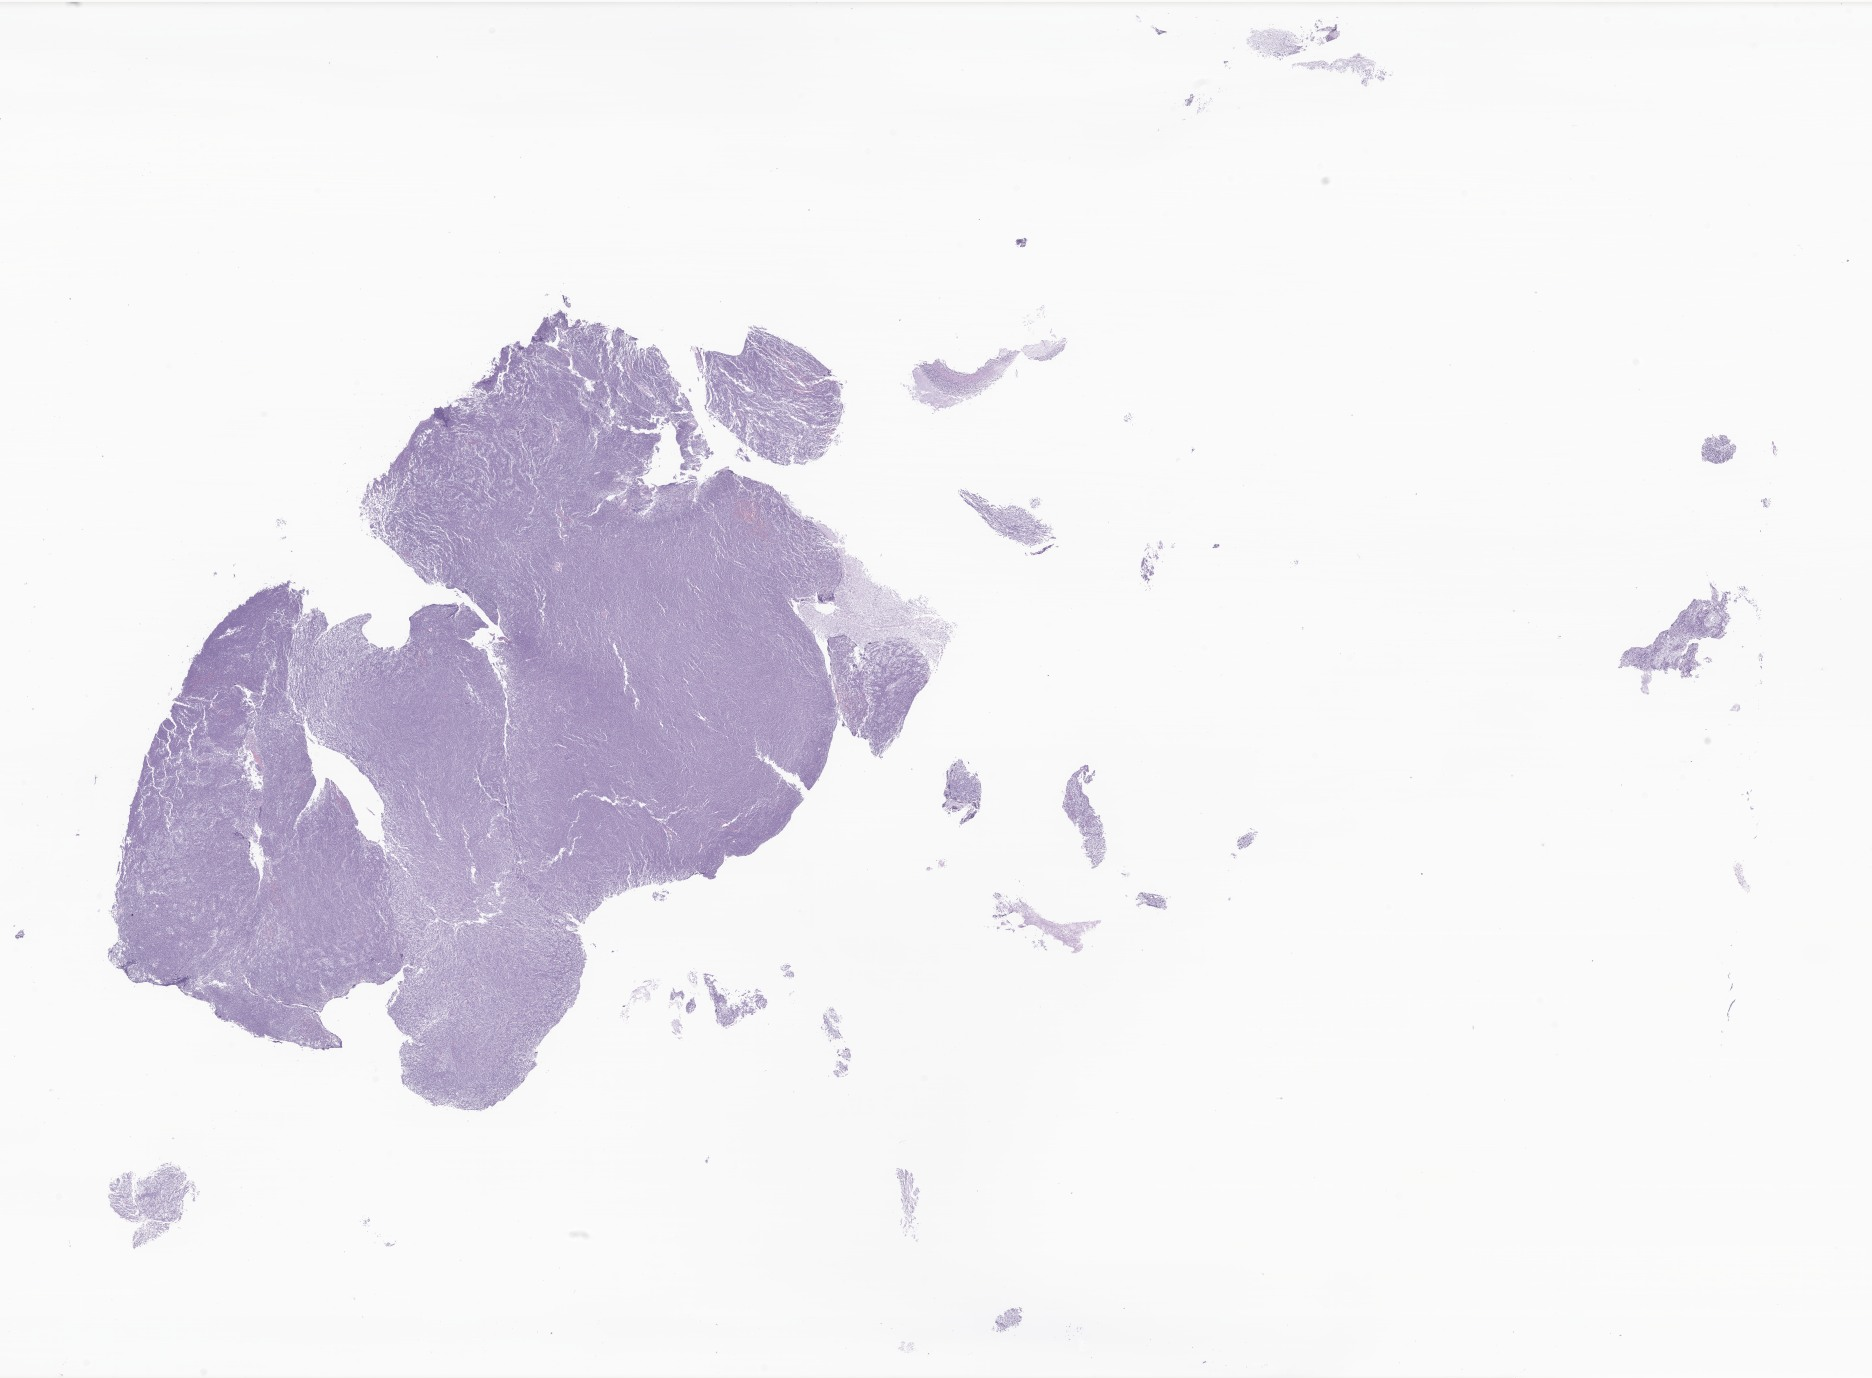
Digitized H&E-stained section of tumor tissue from the brain — whole scanned area (about 31.6 x 23.2 mm) shown as a low-resolution overview; formalin-fixed paraffin-embedded section. Patient female; age 149 months (12 years 5 months).
Diagnosis (ICD-O-3 morphology term): Carcinoma, NOS.